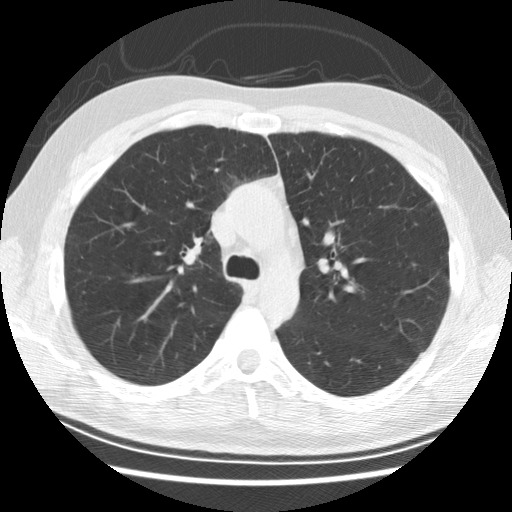
Low-dose screening chest CT, axial slice, first (baseline) screen, lung window (W 1500 / L -600 HU), 2.5 mm slice thickness, standard (soft-tissue) reconstruction kernel (STANDARD). Male, age 57 years at enrolment. Former smoker at enrolment.
Expert-annotated lung lesion, bounding box (x1, y1, x2, y2) in pixels: (164, 220, 224, 277). The screening reader recorded 6 non-calcified nodules or masses ≥4 mm on this exam (right middle lobe, right middle lobe, right lower lobe, right middle lobe, right middle lobe, right lower lobe); which of them this box marks is not recorded. Official screen result: negative screen, minor abnormalities not suspicious for lung cancer. Lung cancer was diagnosed 766 days after this screen (after the second annual screen): adenocarcinoma, NOS, right upper lobe, poorly differentiated (G3), stage IB (AJCC 6th edition), 25 mm at pathology.